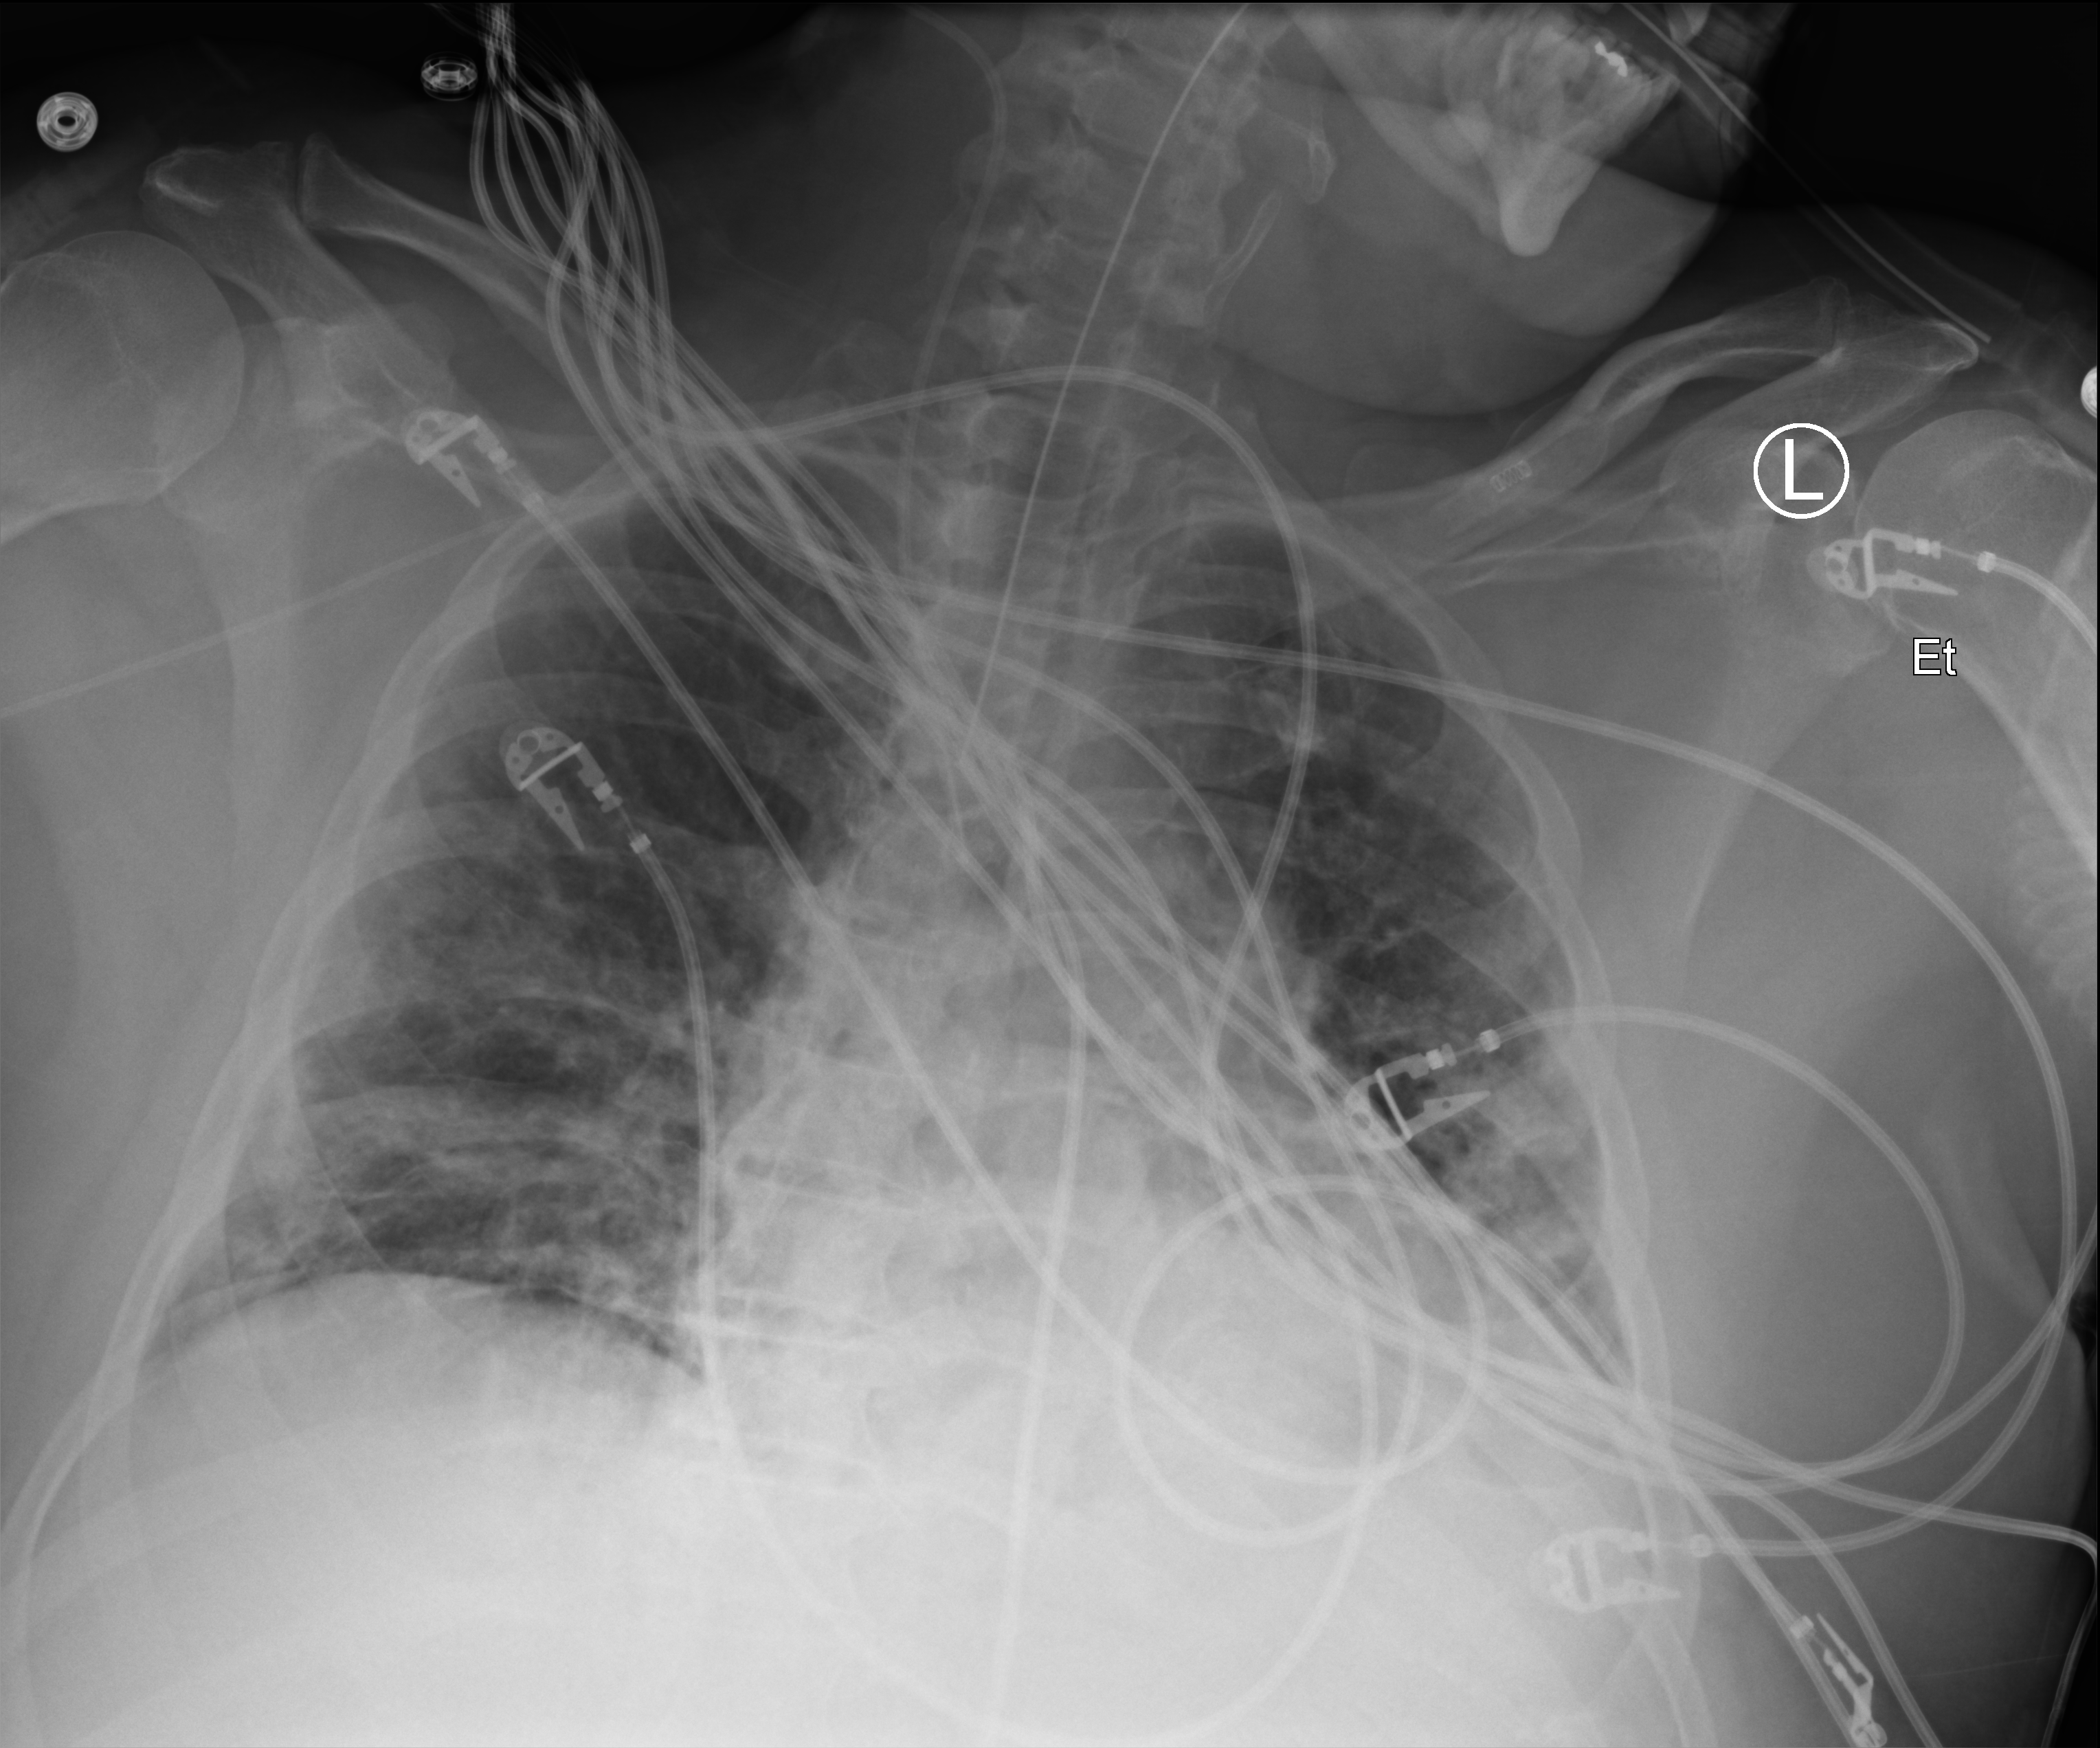
Chest X-ray (portable), anteroposterior (AP) projection. Patient hospitalised with COVID-19; male, aged 18–59 years.
Hospital-stay facts (about this admission, not read from this image; timing relative to this image not recorded):
- mechanically ventilated during this hospital stay: yes
- hypertension (admission record): yes